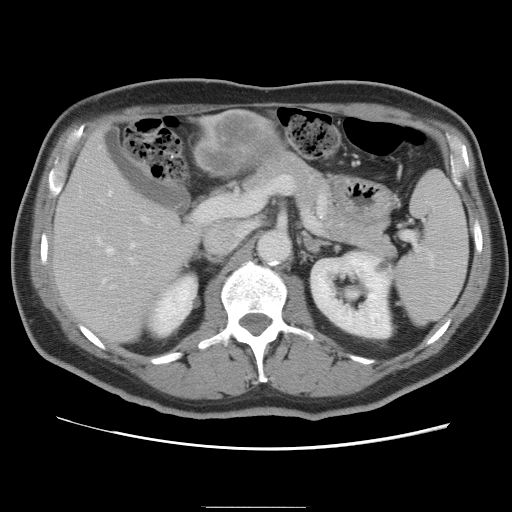
Contrast-enhanced abdominal CT, one axial slice; slice 44 of 87 in the series (ordered by position); 120 kVp; intravenous contrast given; soft-tissue window (W 400 / L 40 HU); 512 × 512 image matrix, field of view 363 × 363 mm. Male patient, age 63 years. Case-level facts recorded for this patient, not image findings: diagnosis: colorectal cancer liver metastases, imaged before liver resection; multiple liver metastases: no; largest metastasis: 9 cm.
Outlined on this slice (outlined manually by an expert reader):
- hepatic veins: bounding box (x1, y1, x2, y2) in pixels: (98, 192, 134, 282)
- liver: (52, 111, 286, 343)
- planned liver remnant (the part of the liver to remain after resection): (52, 148, 198, 344)
- portal vein (with intrahepatic branches): (97, 198, 205, 289)
- liver metastasis: (200, 116, 278, 173)